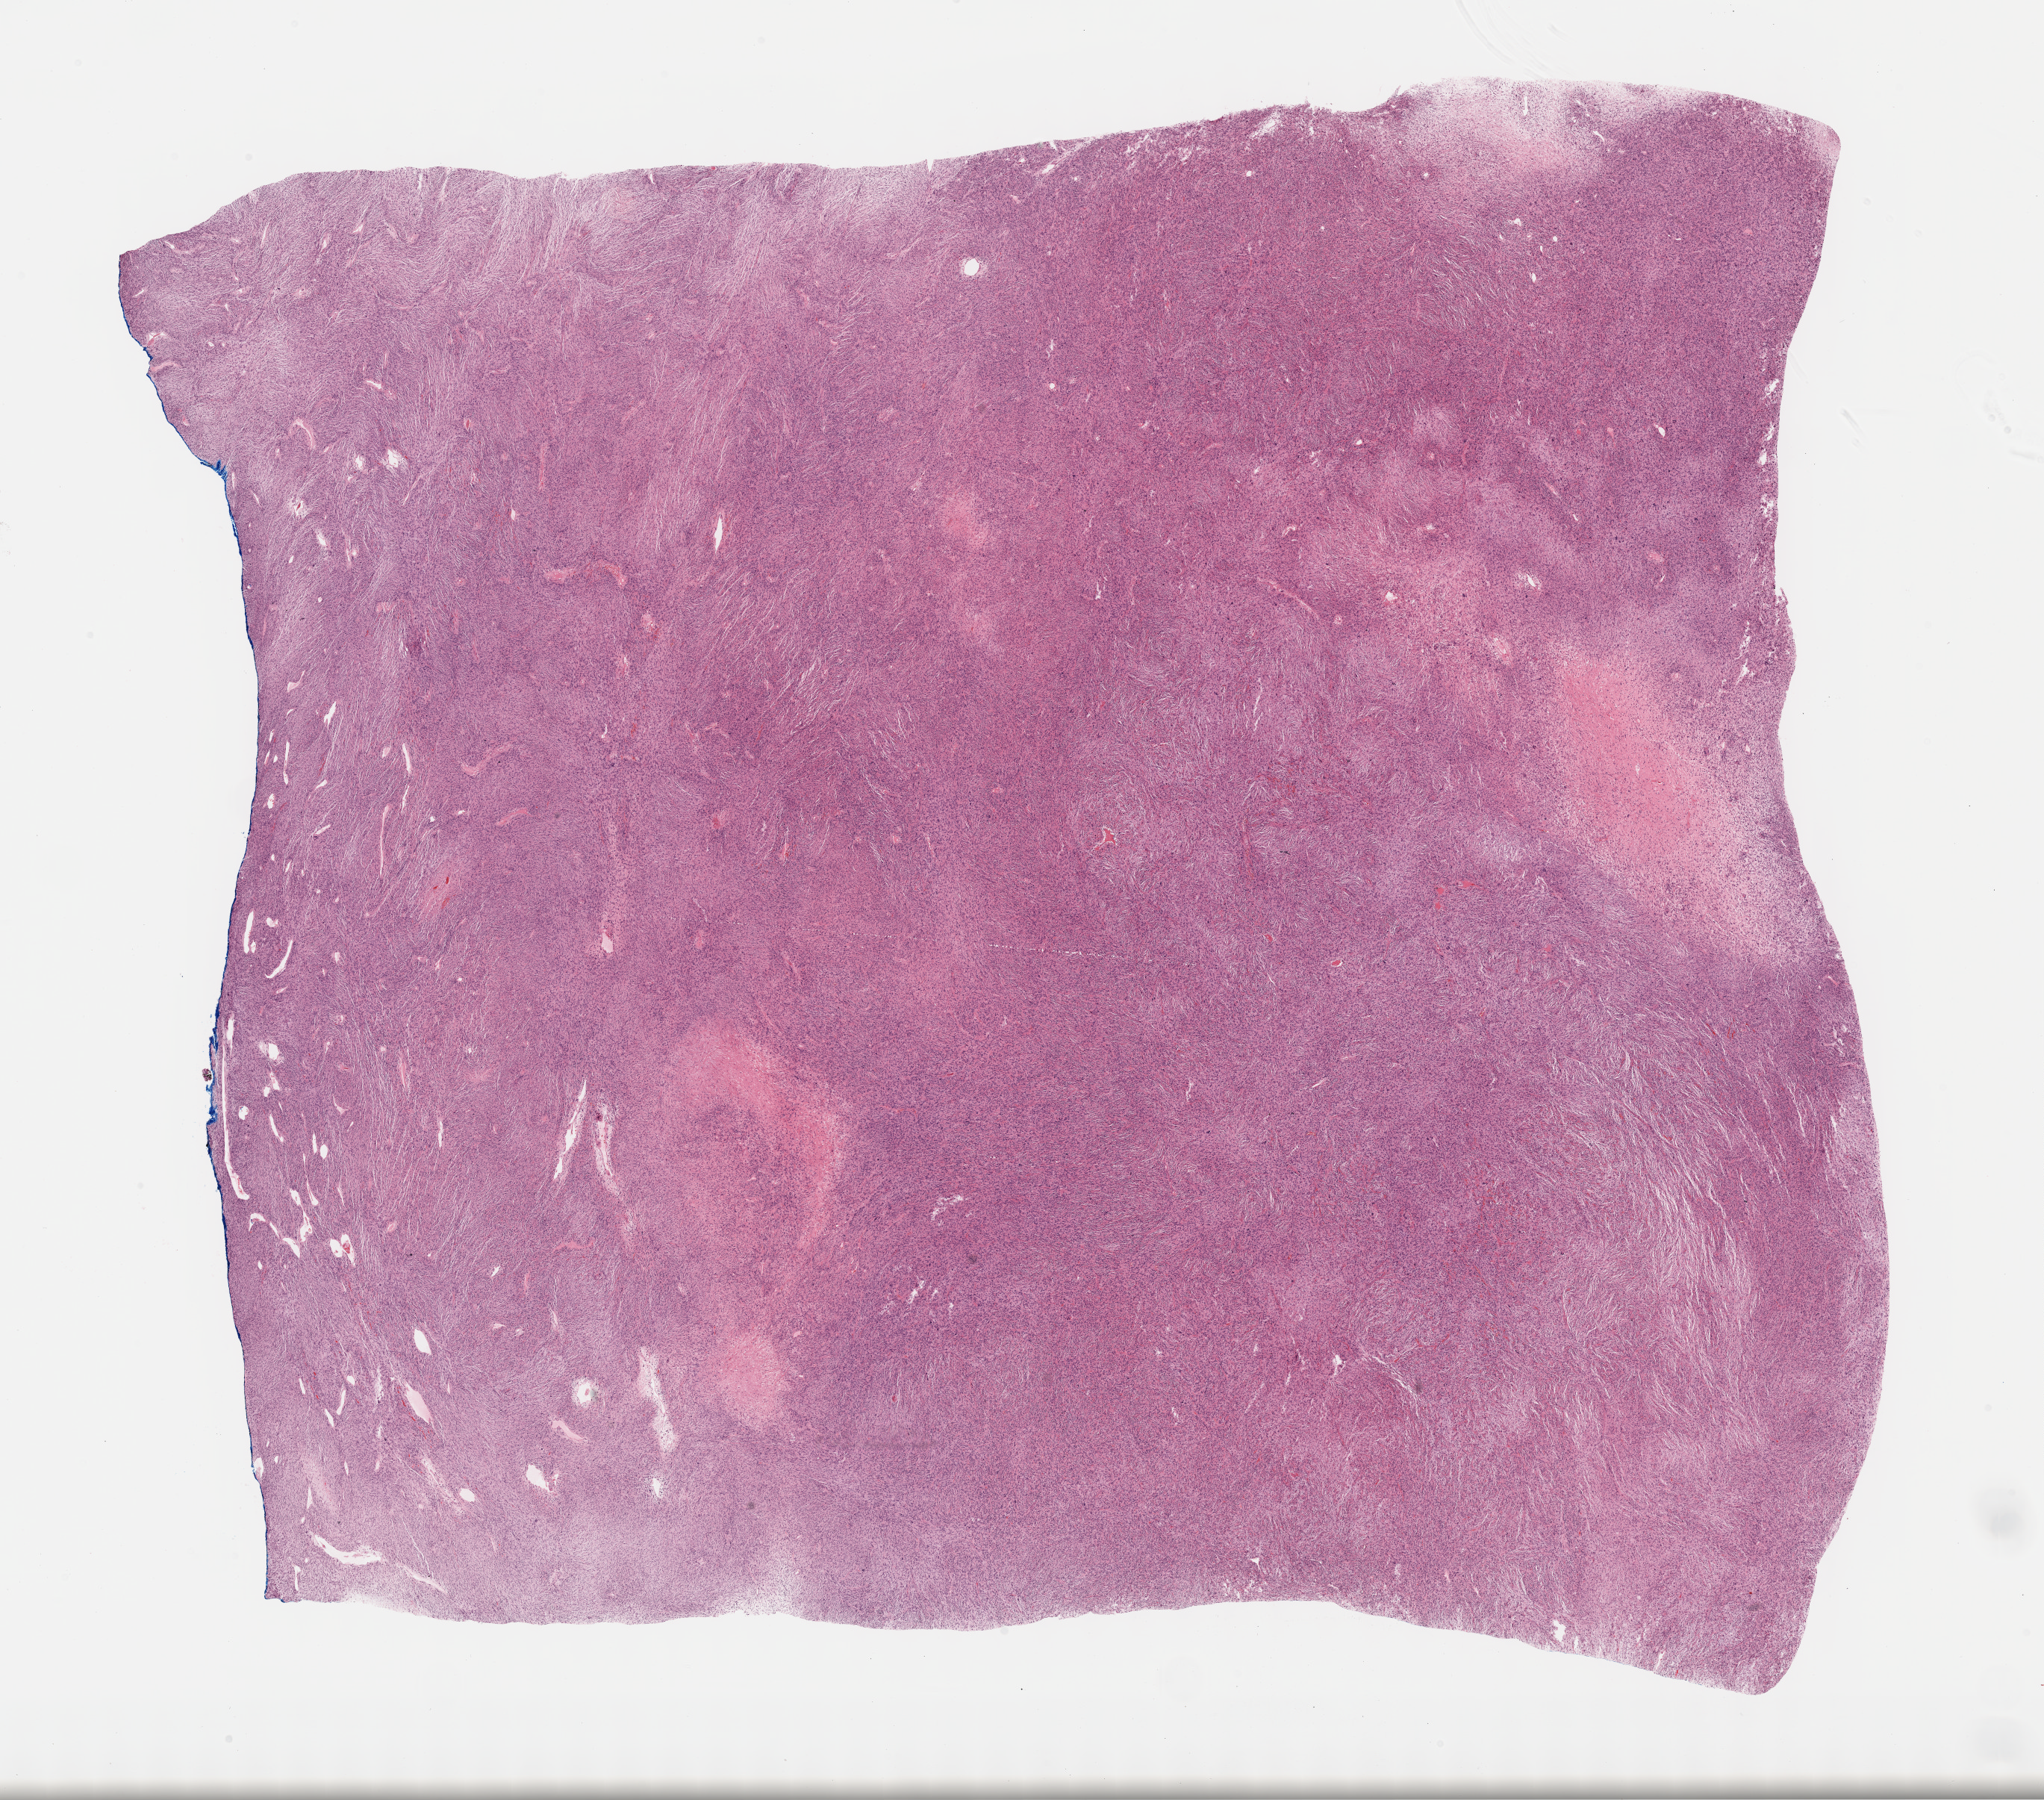
H&E whole-slide image, a low-resolution overview of the entire scanned area, about 22.1 x 19.5 mm; FFPE section; primary tumour sample from the retroperitoneum and peritoneum. Male, age 80 years at initial diagnosis.
- histologic diagnosis: Dedifferentiated liposarcoma (retroperitoneum)